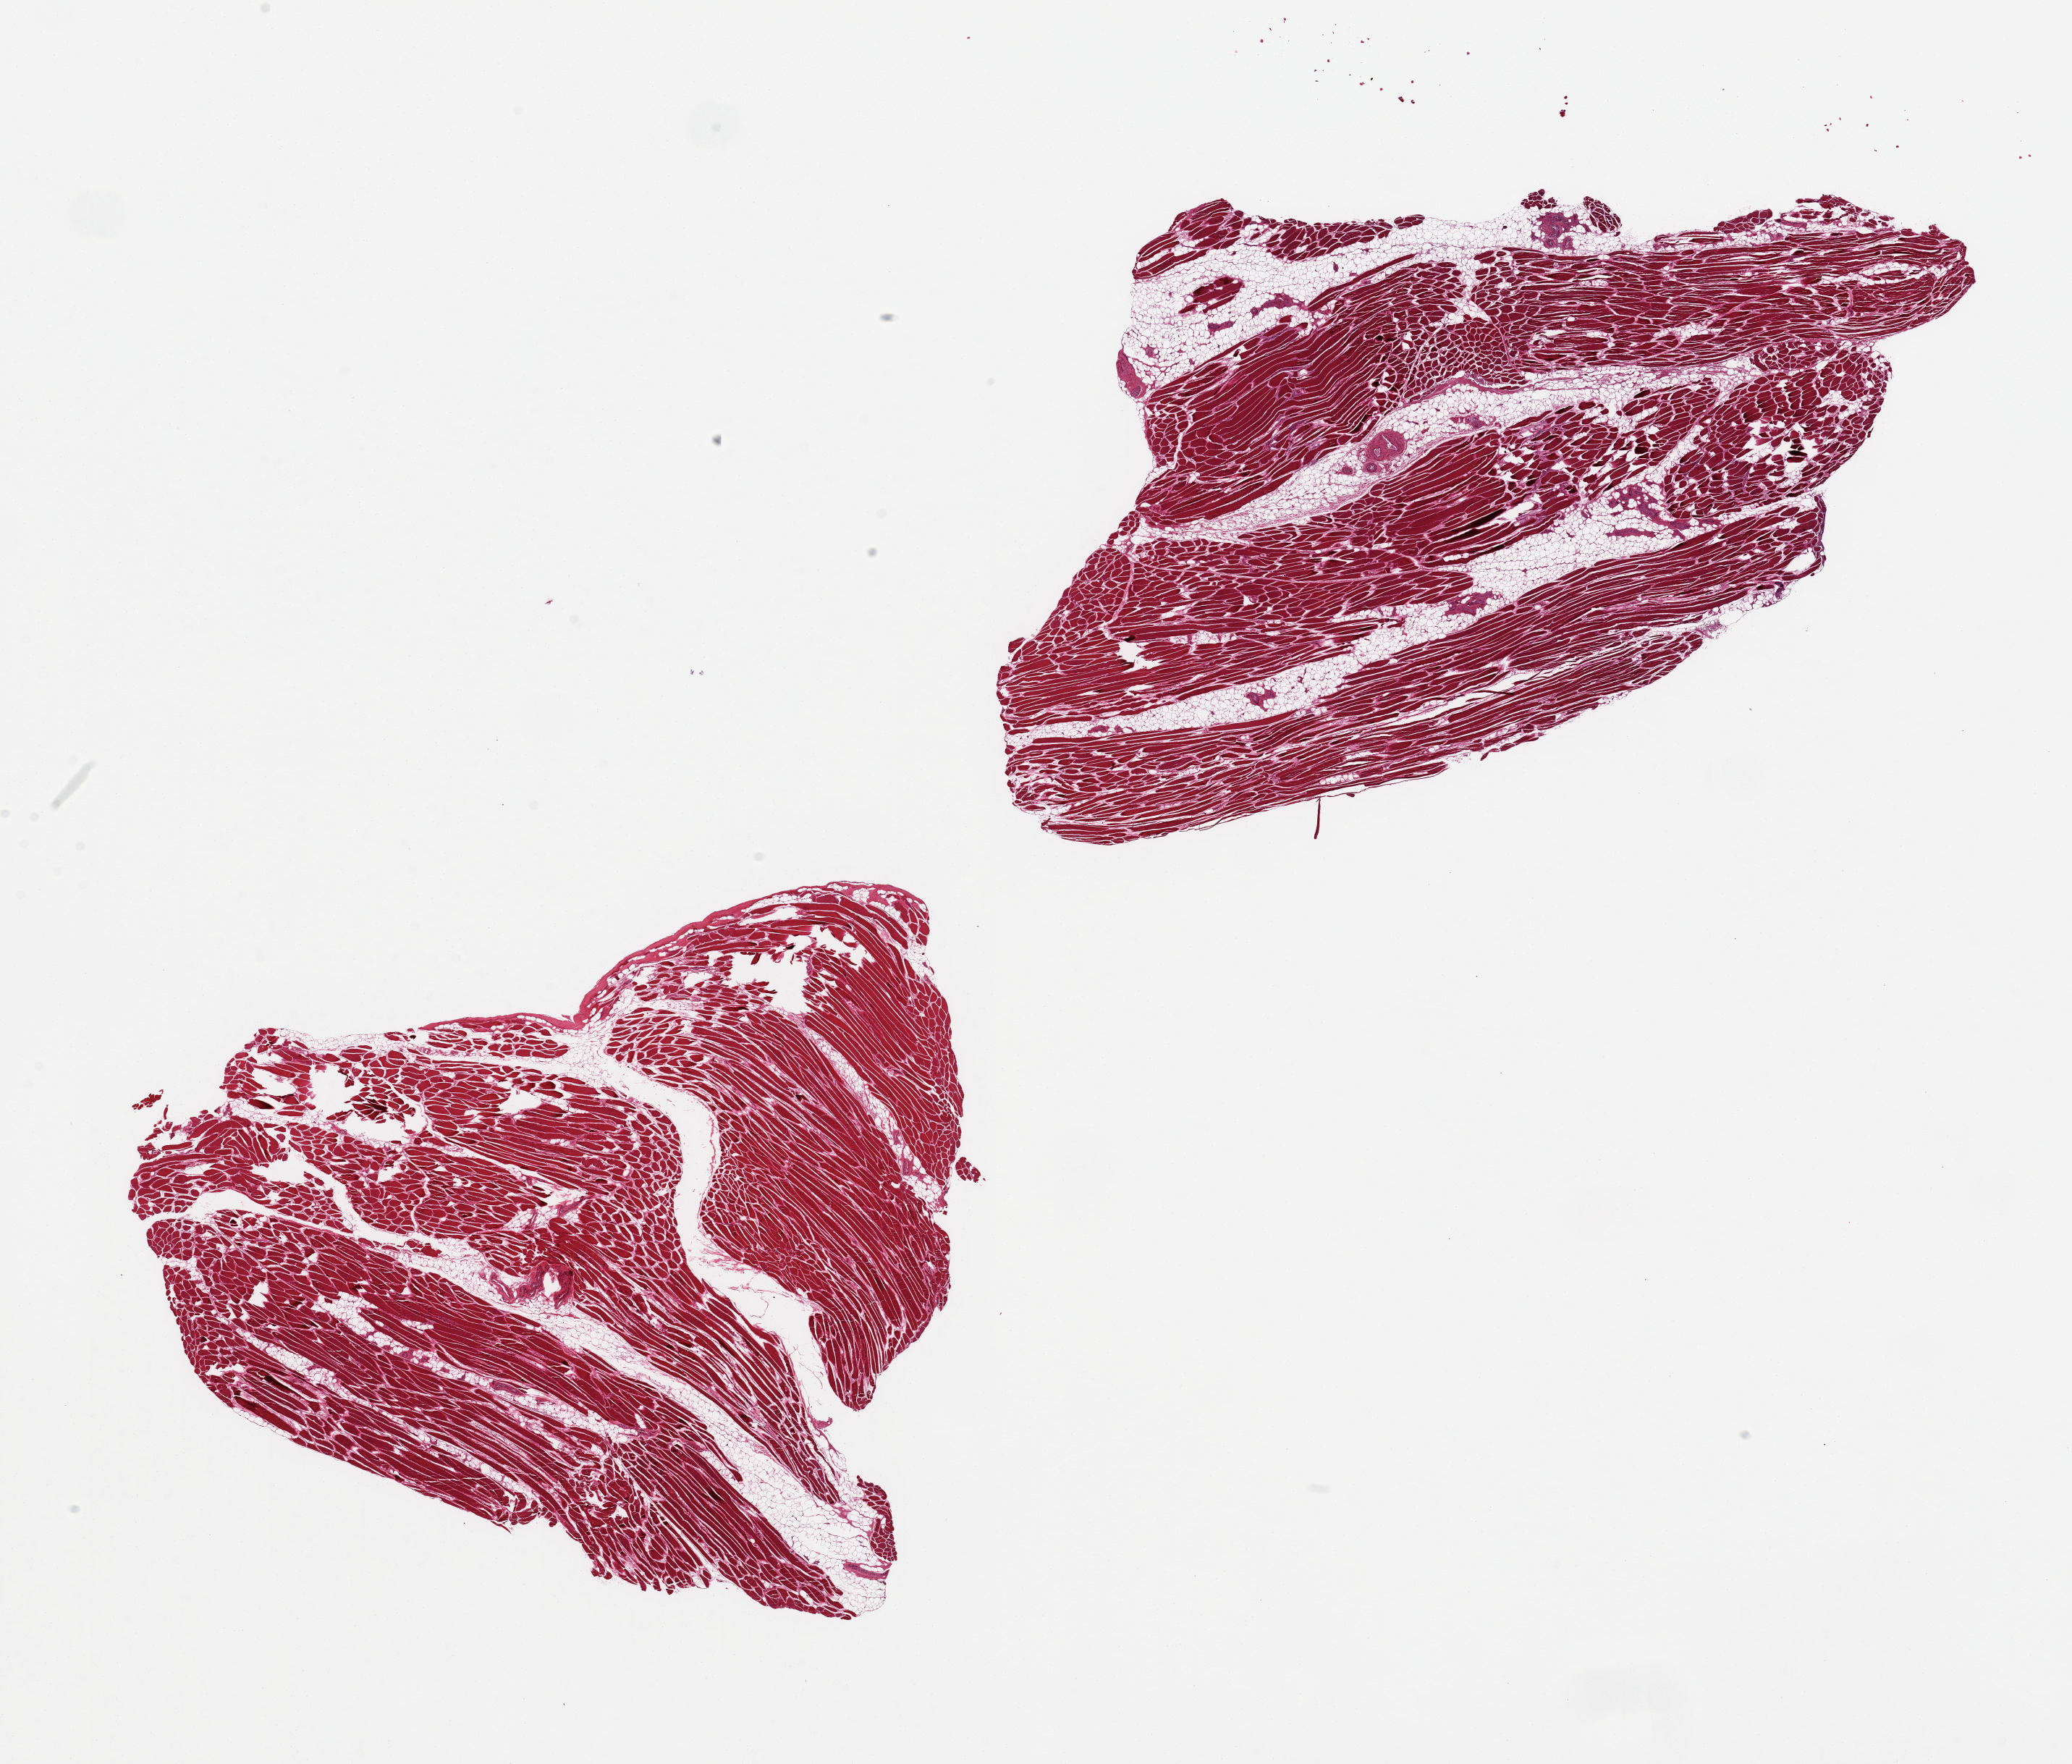
Hematoxylin and eosin (H&E) whole-slide image, low-resolution overview of the scanned area, about 22.6 x 19.3 mm (acquisition: 20x scan). PAXgene-fixed paraffin-embedded (PFPE) section. Section of skeletal muscle (target tissue). Donor tissue sample. Donor sex: female.
Review note (as recorded): 2 pieces; 20% internal fat.